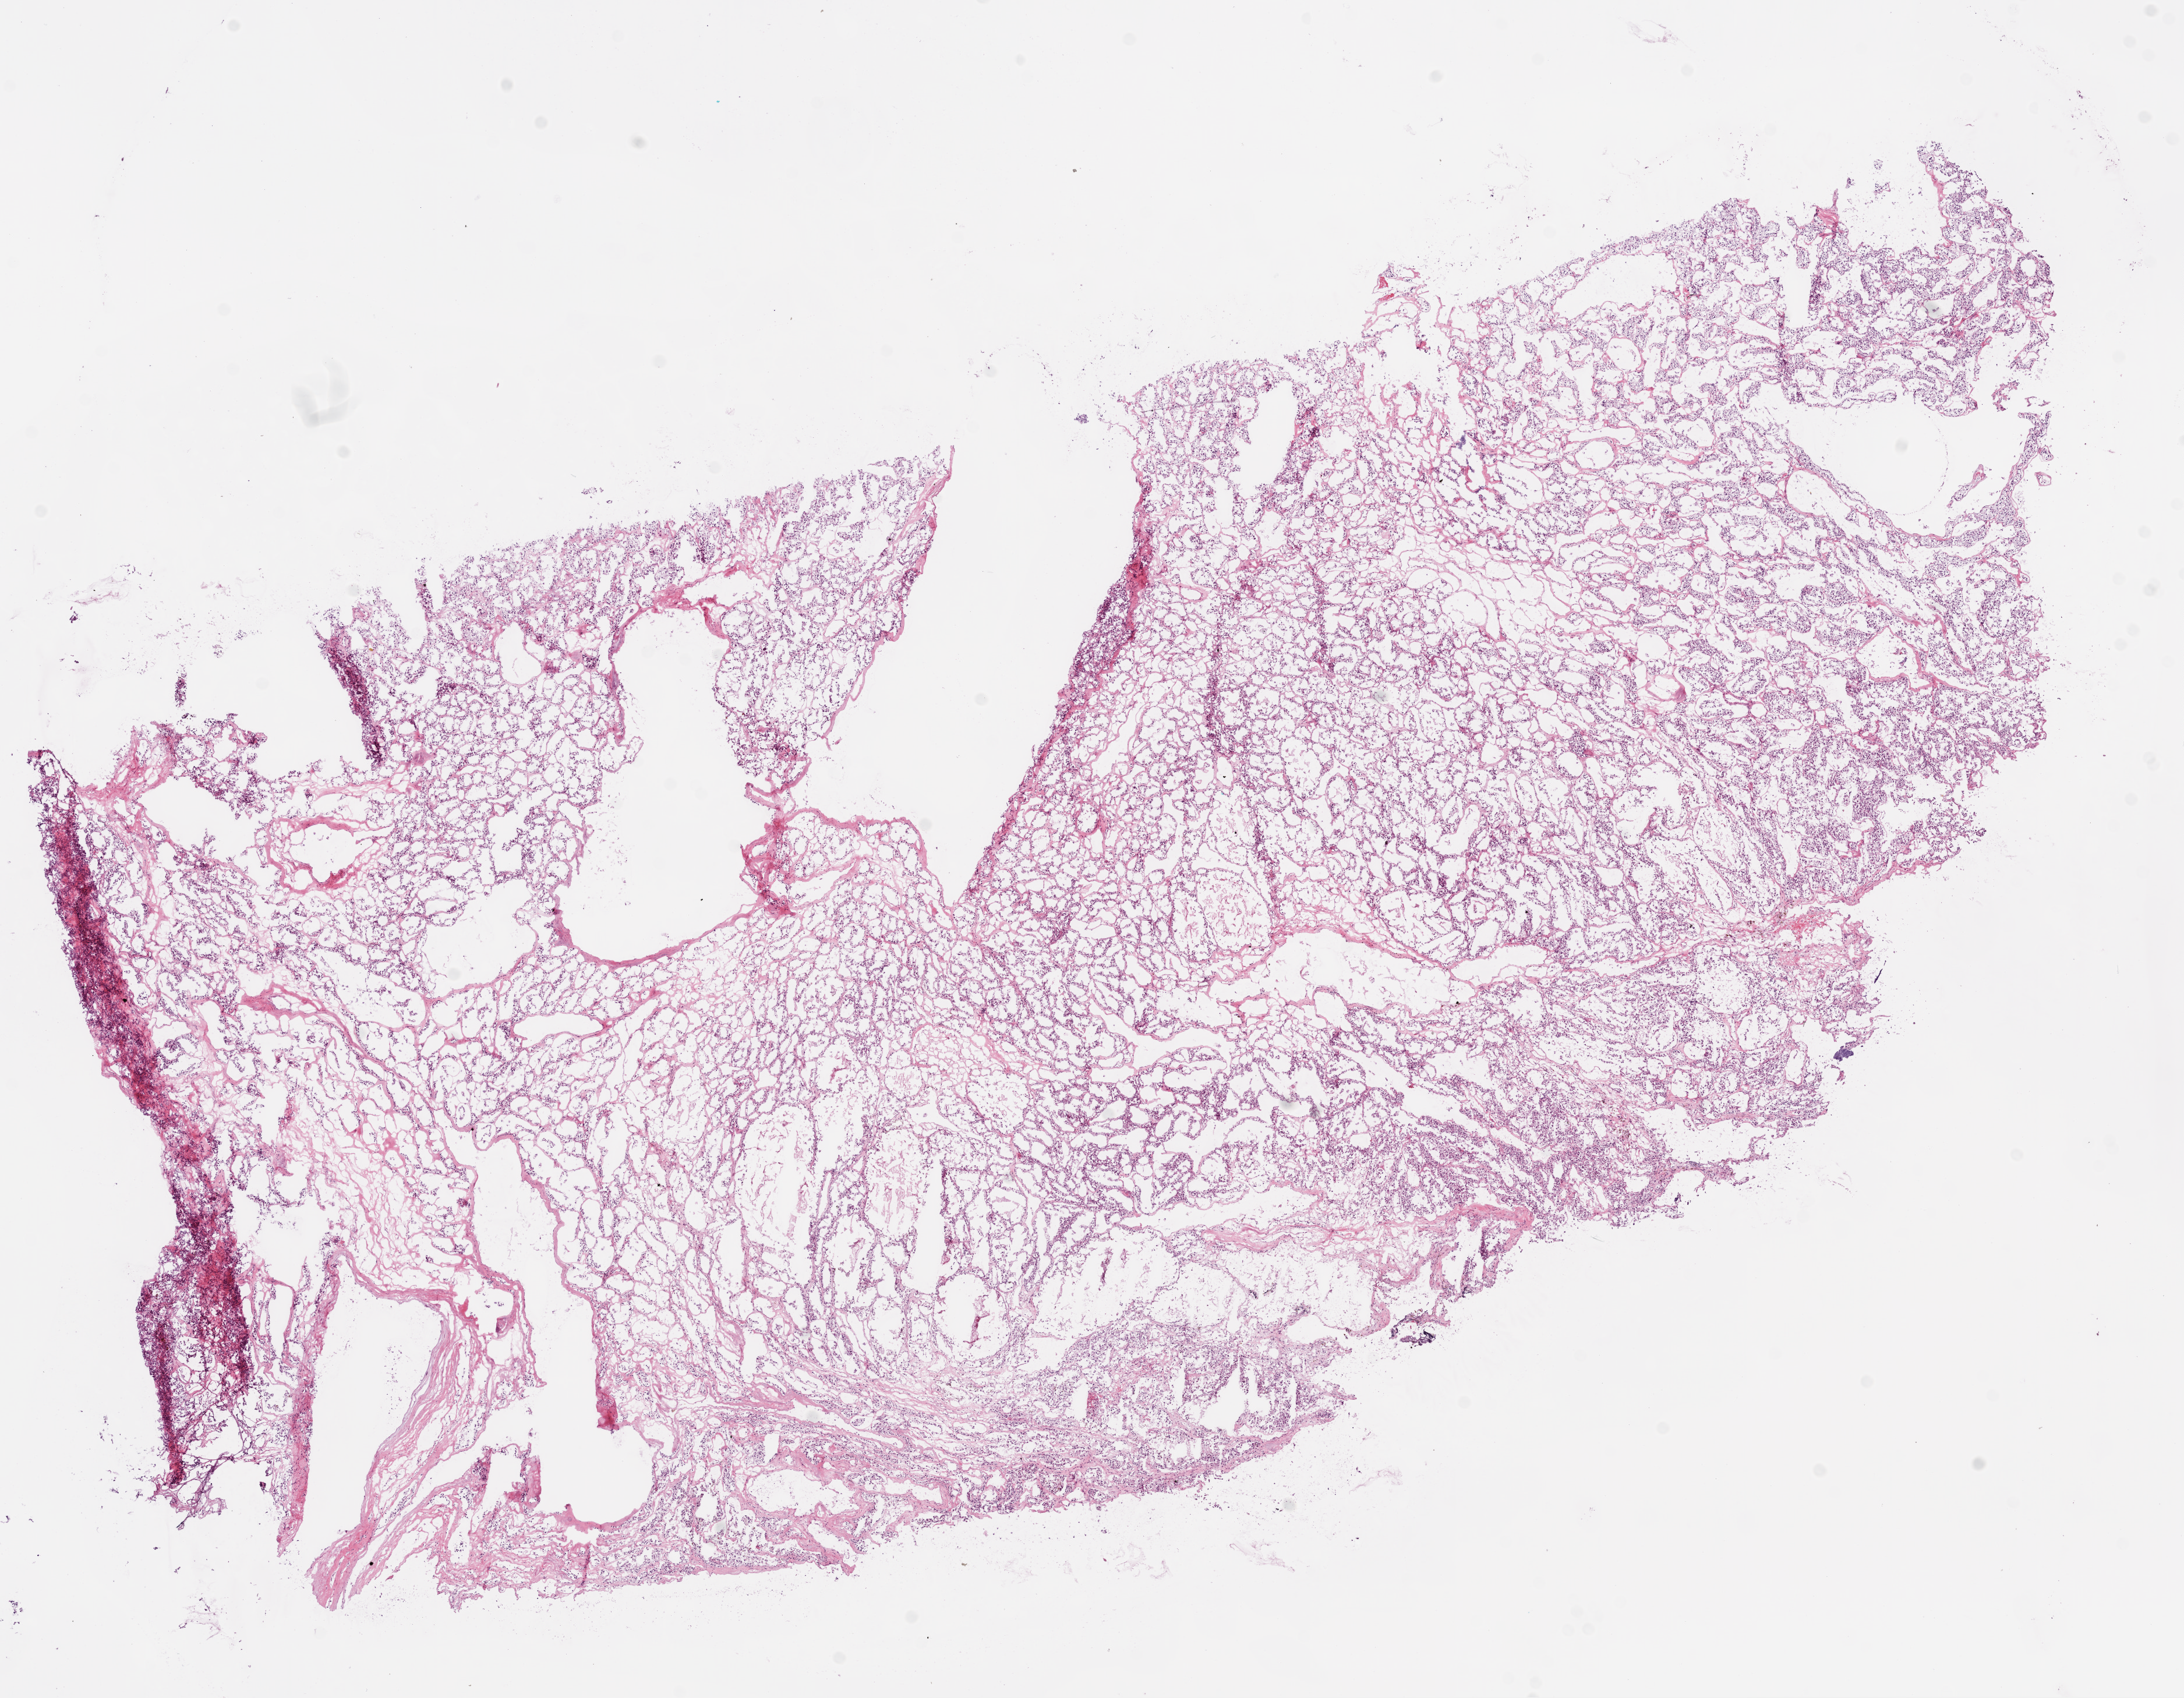
Whole-slide histology image, Hematoxylin and eosin (H&E) stained — low-resolution overview of the scanned area, about 15.0 x 11.7 mm, frozen section from the bottom of the tissue portion, kidney, primary tumour sample. Female patient; age at initial diagnosis 74 years. Histologic grade: G3 (poorly differentiated). Slide review estimates, as recorded: tumour cells 85%, tumour nuclei 80%, normal cells 0%, stromal cells 15%, necrosis 0%.
Pathologic diagnosis: Clear cell adenocarcinoma, NOS. AJCC pathologic stage: I.